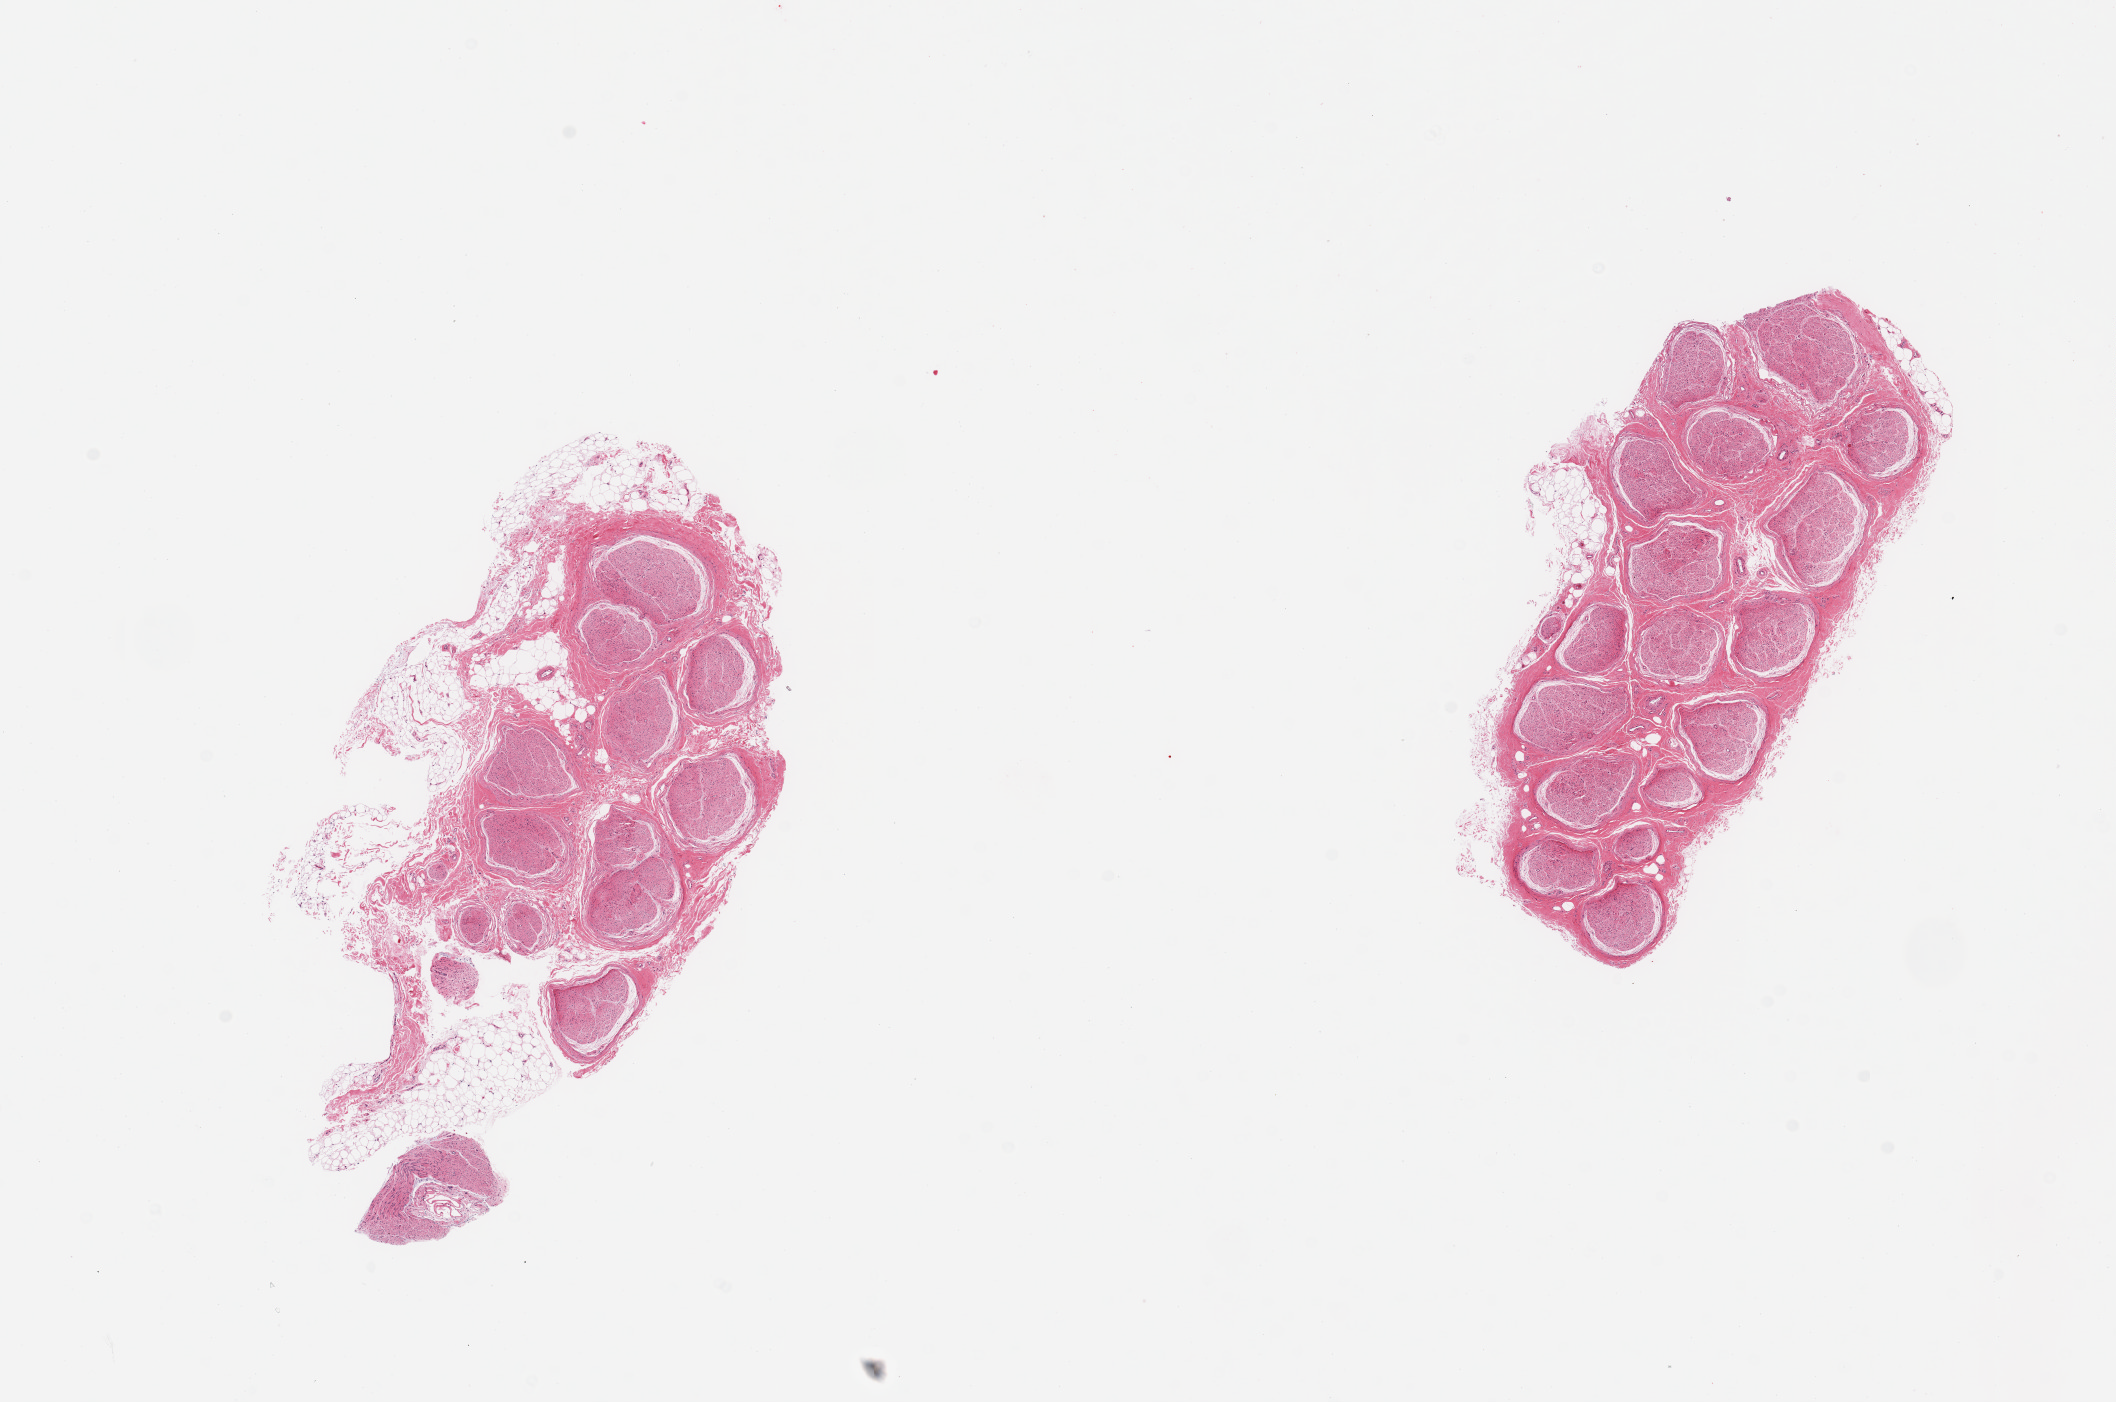
Whole-slide image, H&E stain — whole scanned area (about 16.7 x 11.1 mm) shown as a low-resolution overview, PAXgene-fixed paraffin-embedded (PFPE) section, section of tibial nerve (target tissue), donor tissue sample. Donor: male.
- review note (as recorded): 2 pieces, nubbins of adherent fat up to ~1mm